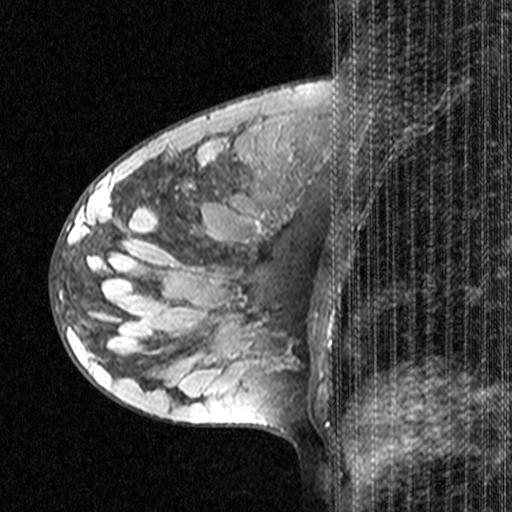
Breast MRI (dynamic contrast-enhanced), one sagittal slice. Position 18 of 44 along the scan axis. Dynamic contrast-enhanced study with each time point stored as its own series, time point 2 of 3 at this slice position (early post-contrast, ordered by acquisition time). 1.5 T. TE 4.5 ms, TR 11 ms. 3 mm slice thickness. 512 × 512 image matrix. Female patient, age 28 years. From the clinical record (not read from this slice): setting: breast cancer imaged before/during neoadjuvant chemotherapy; receptor status: HR-positive, HER2-negative.
Structures marked on this image (semi-automatically segmented with operator editing):
- analysis volume of interest (the breast-tissue region the enhancement analysis was run in; not a lesion): bounding box <51,182,151,283> (left, top, right, bottom; pixels)
- tumour enhancement mask (voxels above the 90 % enhancement threshold inside the analysis volume of interest): <79,182,101,214>